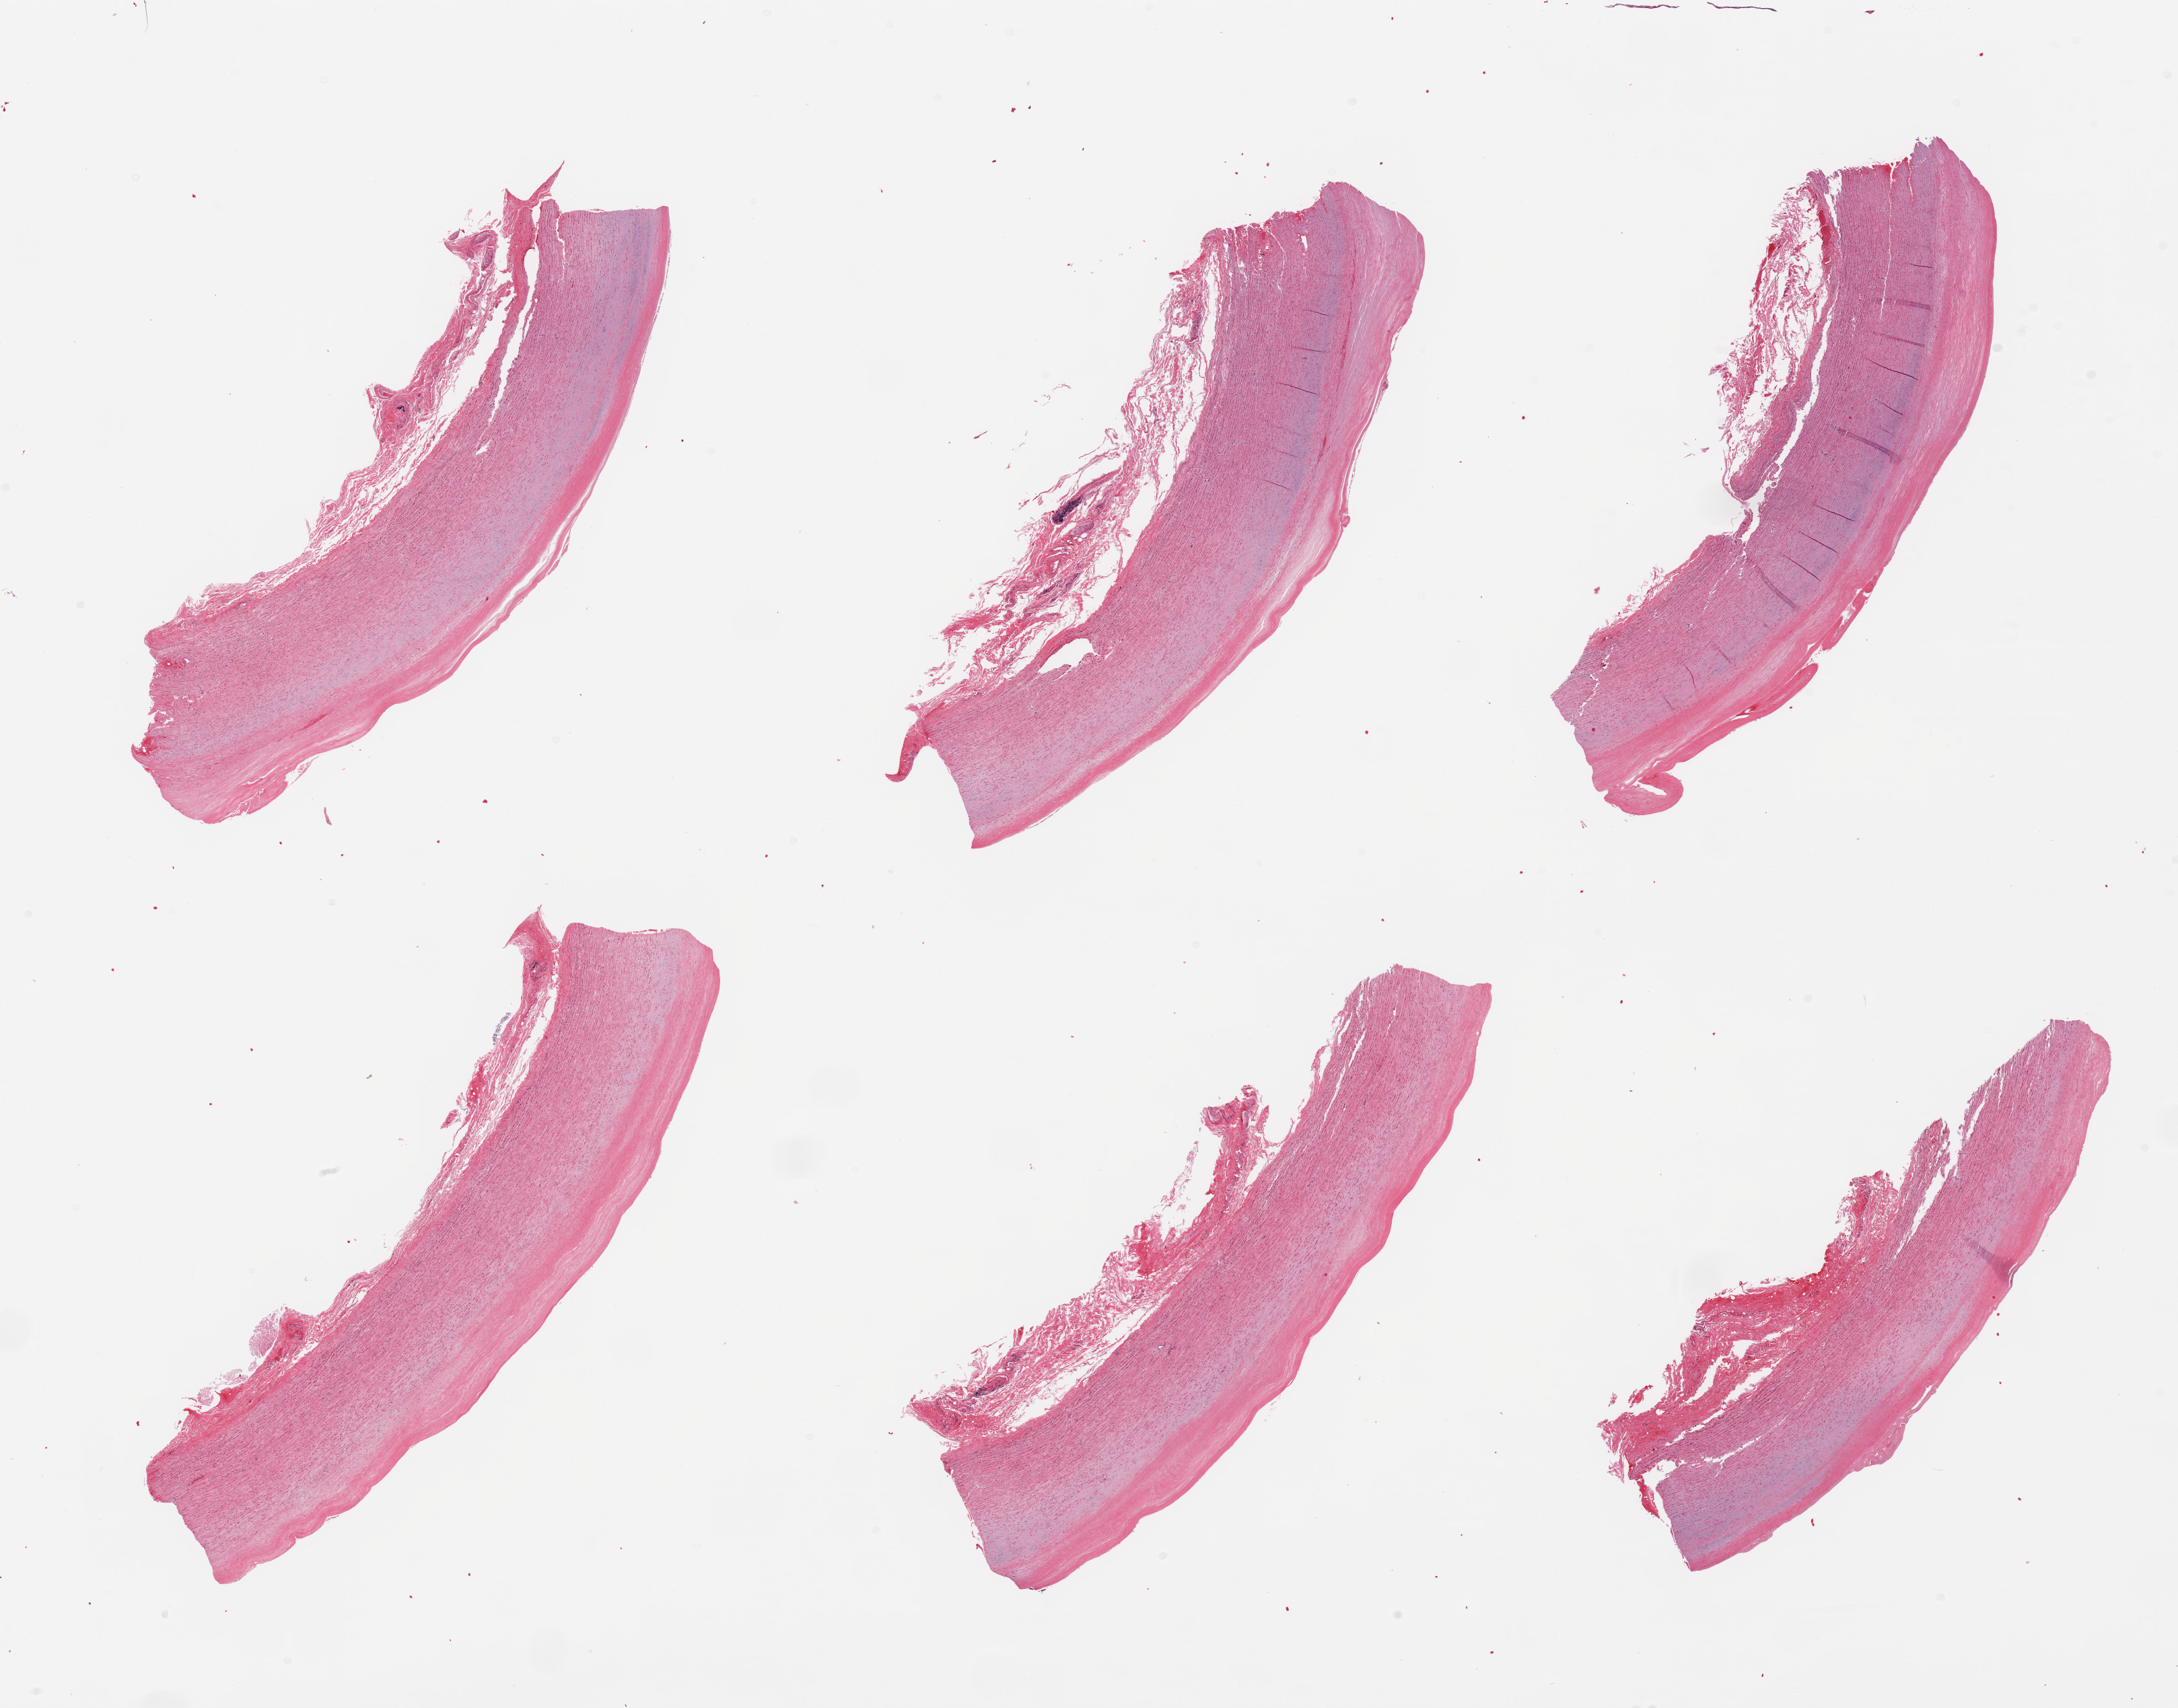
Hematoxylin and eosin (H&E) whole-slide image, a low-resolution overview of the entire scanned area, about 25.6 x 20.1 mm; PAXgene-fixed paraffin-embedded (PFPE) section; section of aorta (target tissue); donor tissue sample. Donor sex: female.
• pathologist's review note for this sample: 6 pieces; moderate linear plaques; focally thickened adventitia up to 0.6mm